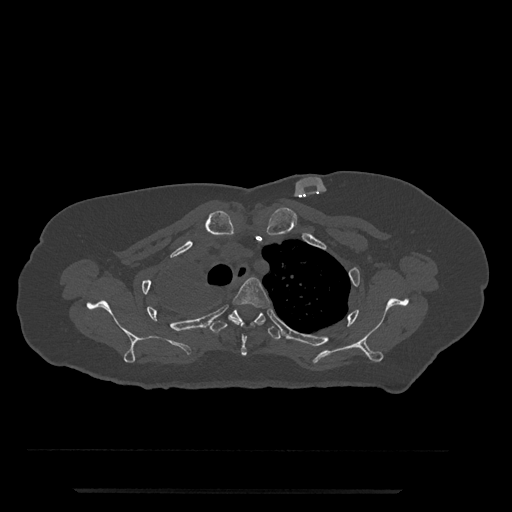
CT including the spine, one axial slice; slice 614 of 797 in the series (ordered by position); bone window (W 1800 / L 400 HU); 512 × 512 image matrix, field of view 440 × 440 mm. Female patient, age 51 years. From the clinical record (not read from this slice): primary cancer: neuro.
Annotated regions visible in this slice (semi-automatic segmentation, software-assisted and operator-edited):
- T3 vertebra: bounding box (x1, y1, x2, y2) in pixels: (233, 277, 270, 356)
- T4 vertebra: (209, 309, 281, 340)